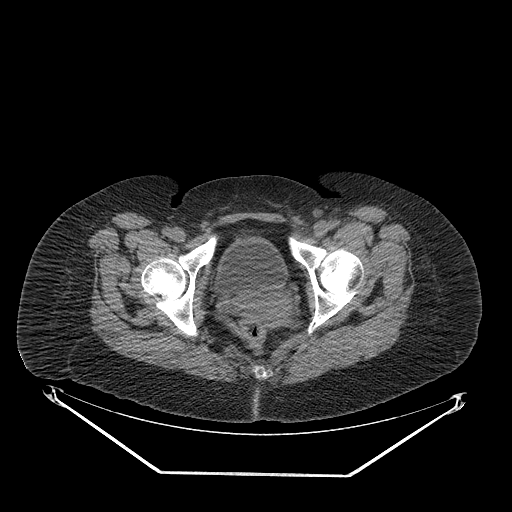
CT of an extremity soft-tissue mass (from a PET/CT study), one axial slice; slice 59 of 267 in the series (ordered by position); reconstruction kernel STANDARD; 140 kVp; soft-tissue window (W 400 / L 40 HU); 3.75 mm slice thickness; 512 × 512 image matrix, field of view 500 × 500 mm. Female patient. From the clinical record (not read from this slice): histological type: myxofibrosarcoma; grade: intermediate; site of the primary tumour: left thigh.
Structures marked on this image (expert contour drawn on MRI and transferred to this co-registered scan by the dataset authors):
- gross tumour volume including surrounding oedema: box from (x=299, y=226) to (x=350, y=248) px